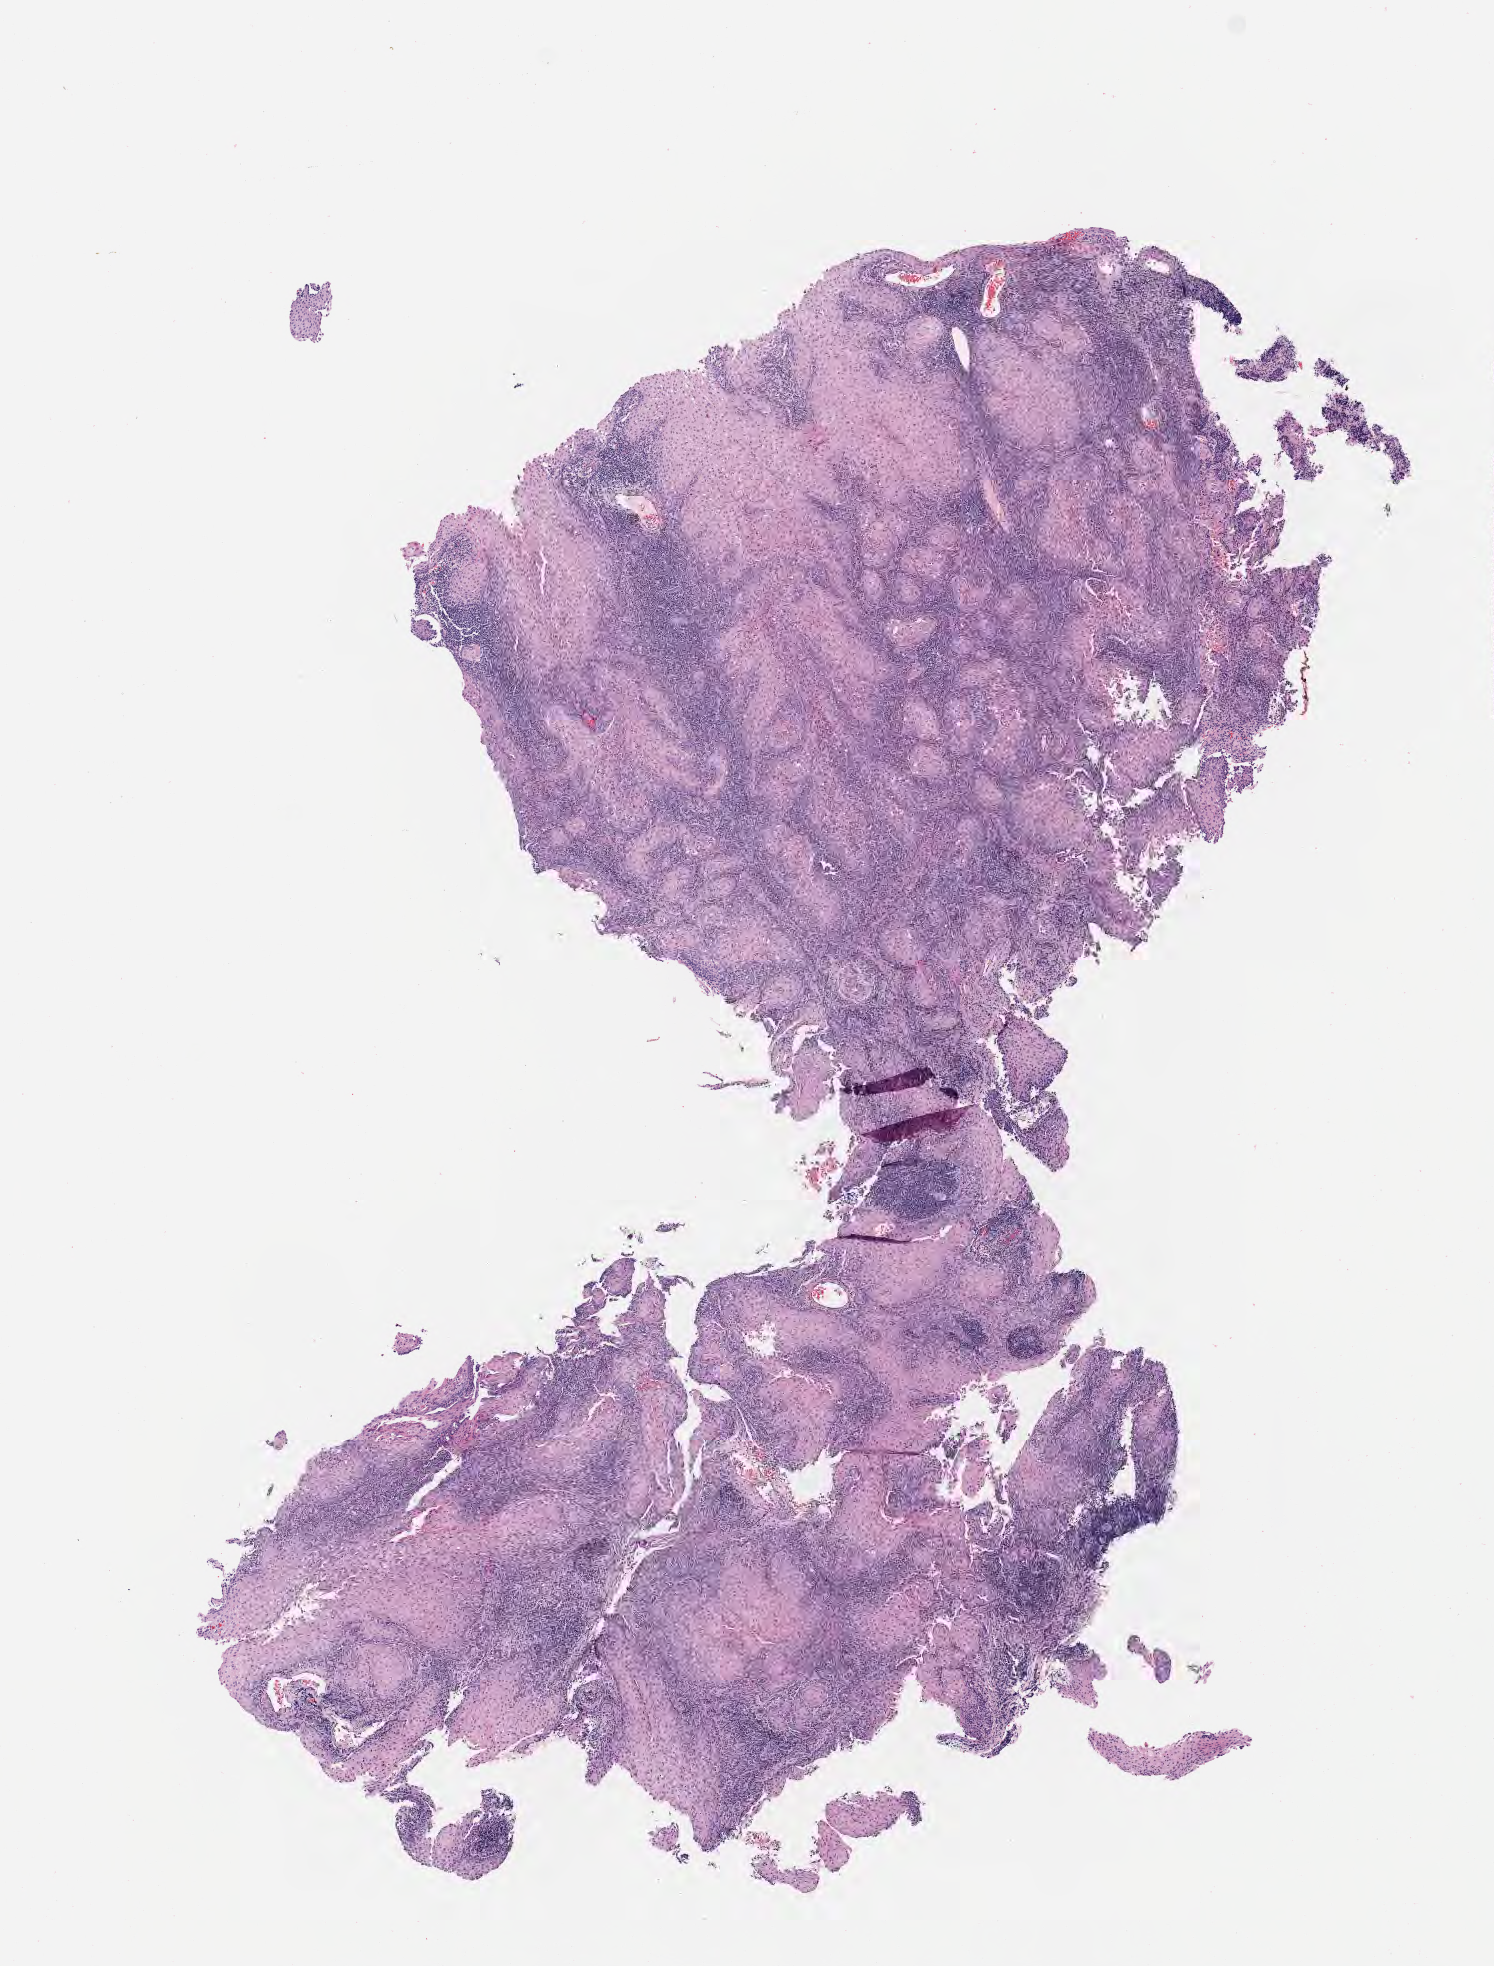
Digitized H&E-stained section — low-resolution overview of the scanned area, about 6.0 x 7.9 mm; specimen: tumor tissue; site: cervix. Female patient, 57 years old.
• histologic diagnosis: Squamous cell carcinoma, large cell, nonkeratinizing, NOS